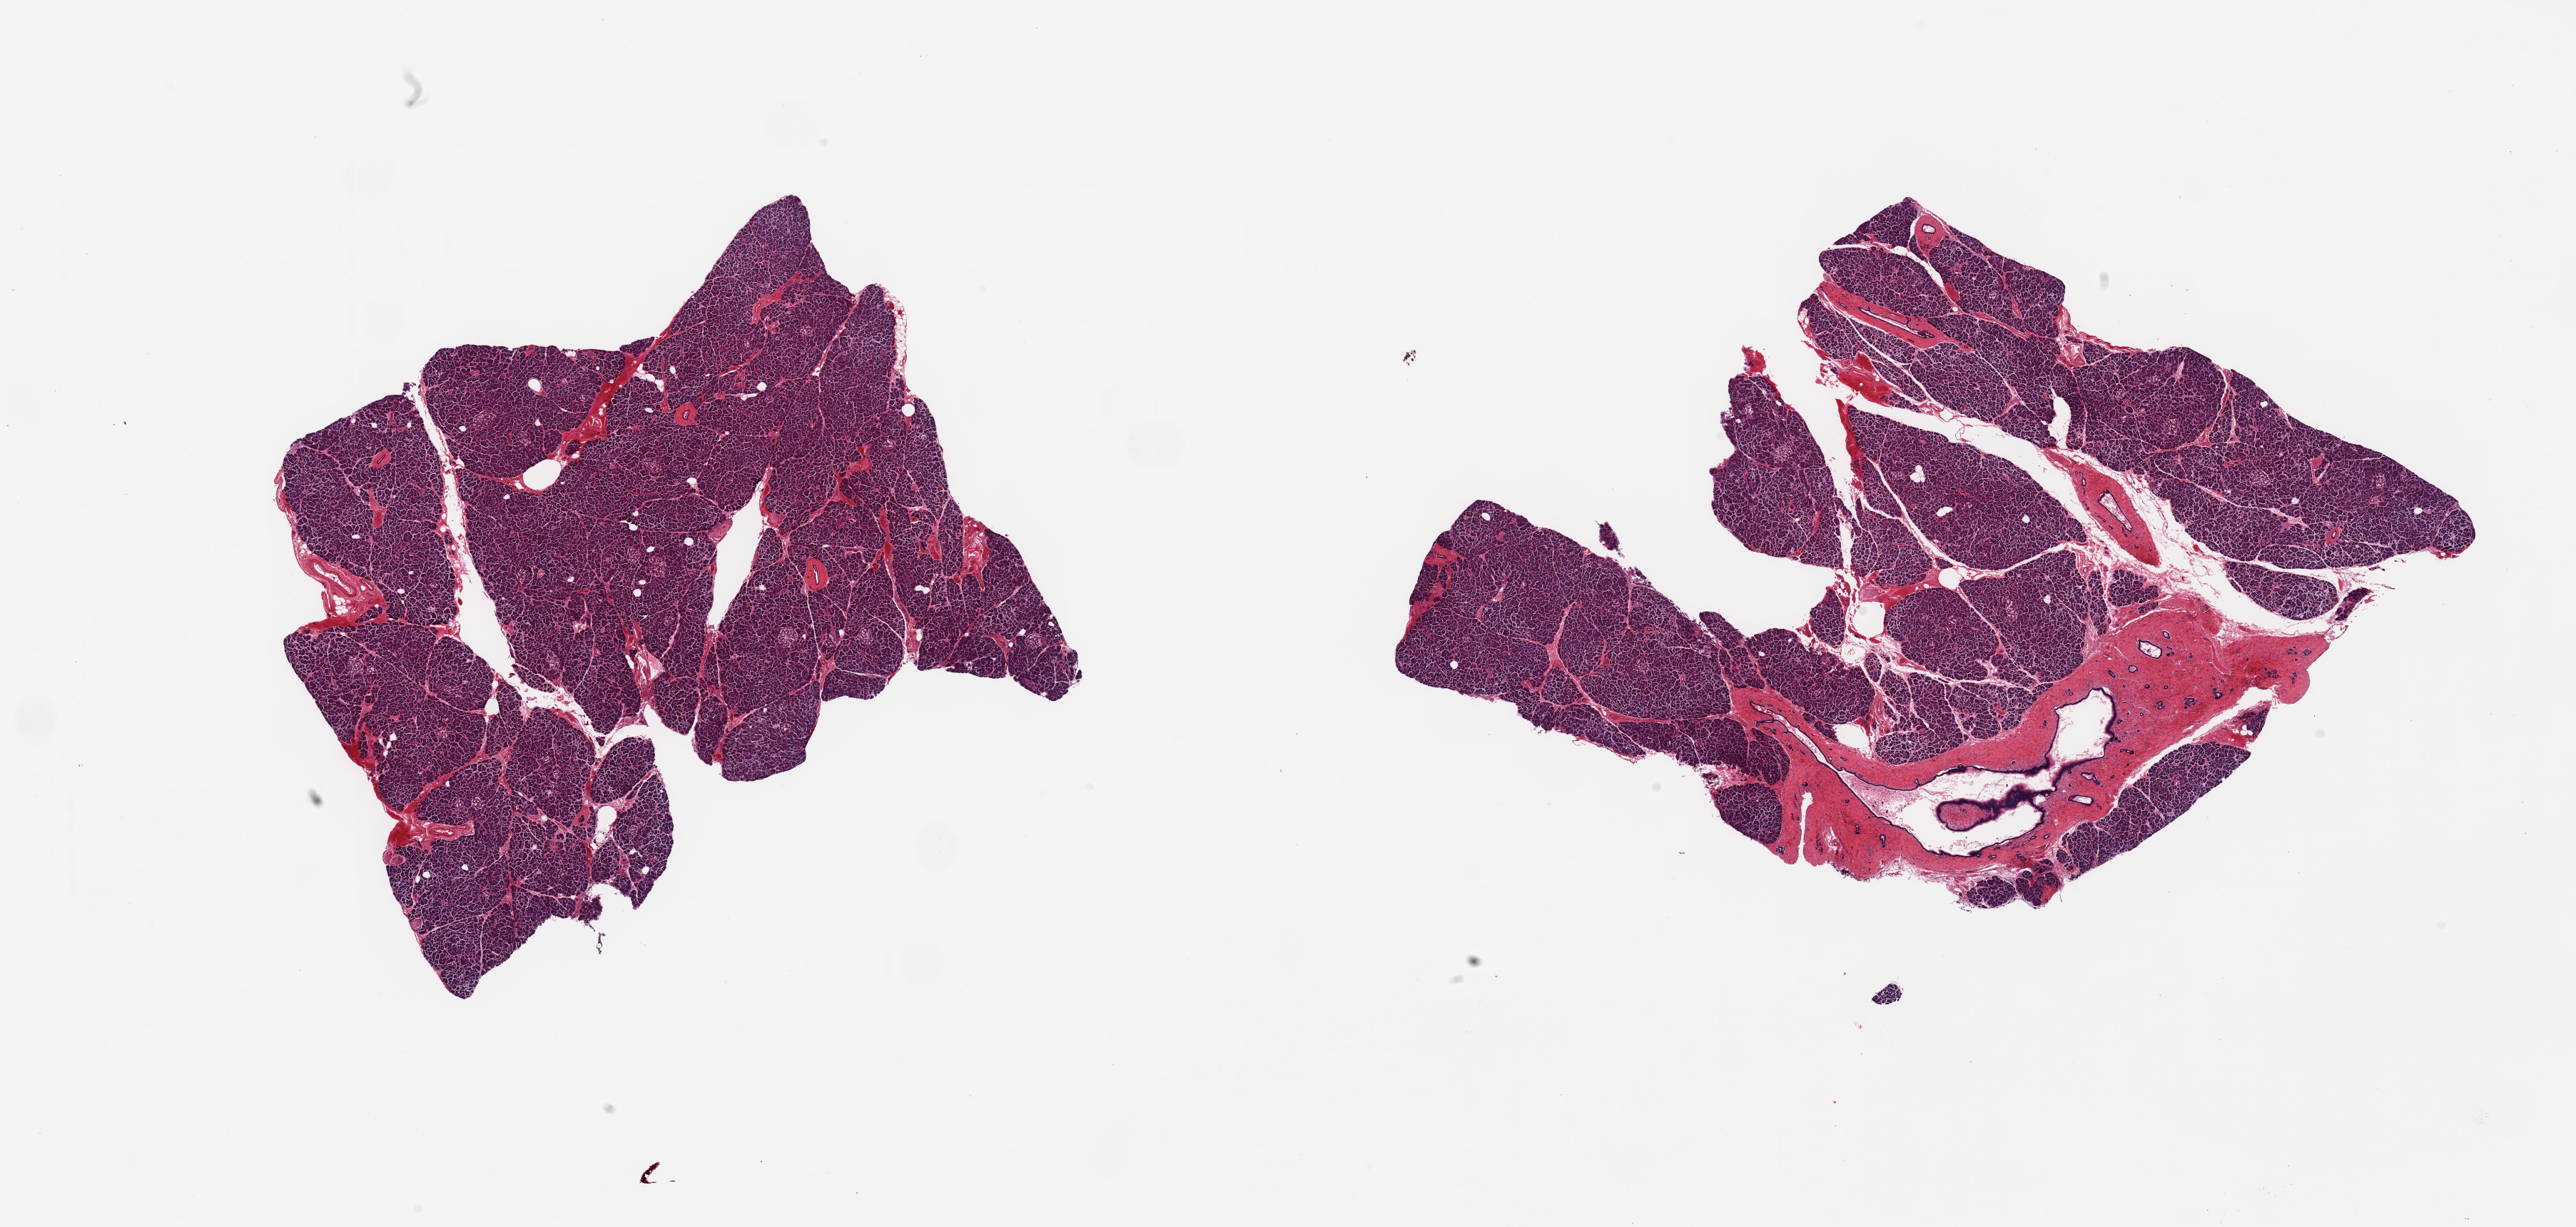
Digitized H&E-stained section, whole scanned area (about 28.5 x 13.6 mm) shown as a low-resolution overview. PAXgene-fixed paraffin-embedded (PFPE) section. Target tissue: pancreas. Donor tissue sample.
* pathologist's review note for this sample: 2 pieces; large ducts comprise 25% of 1 piece